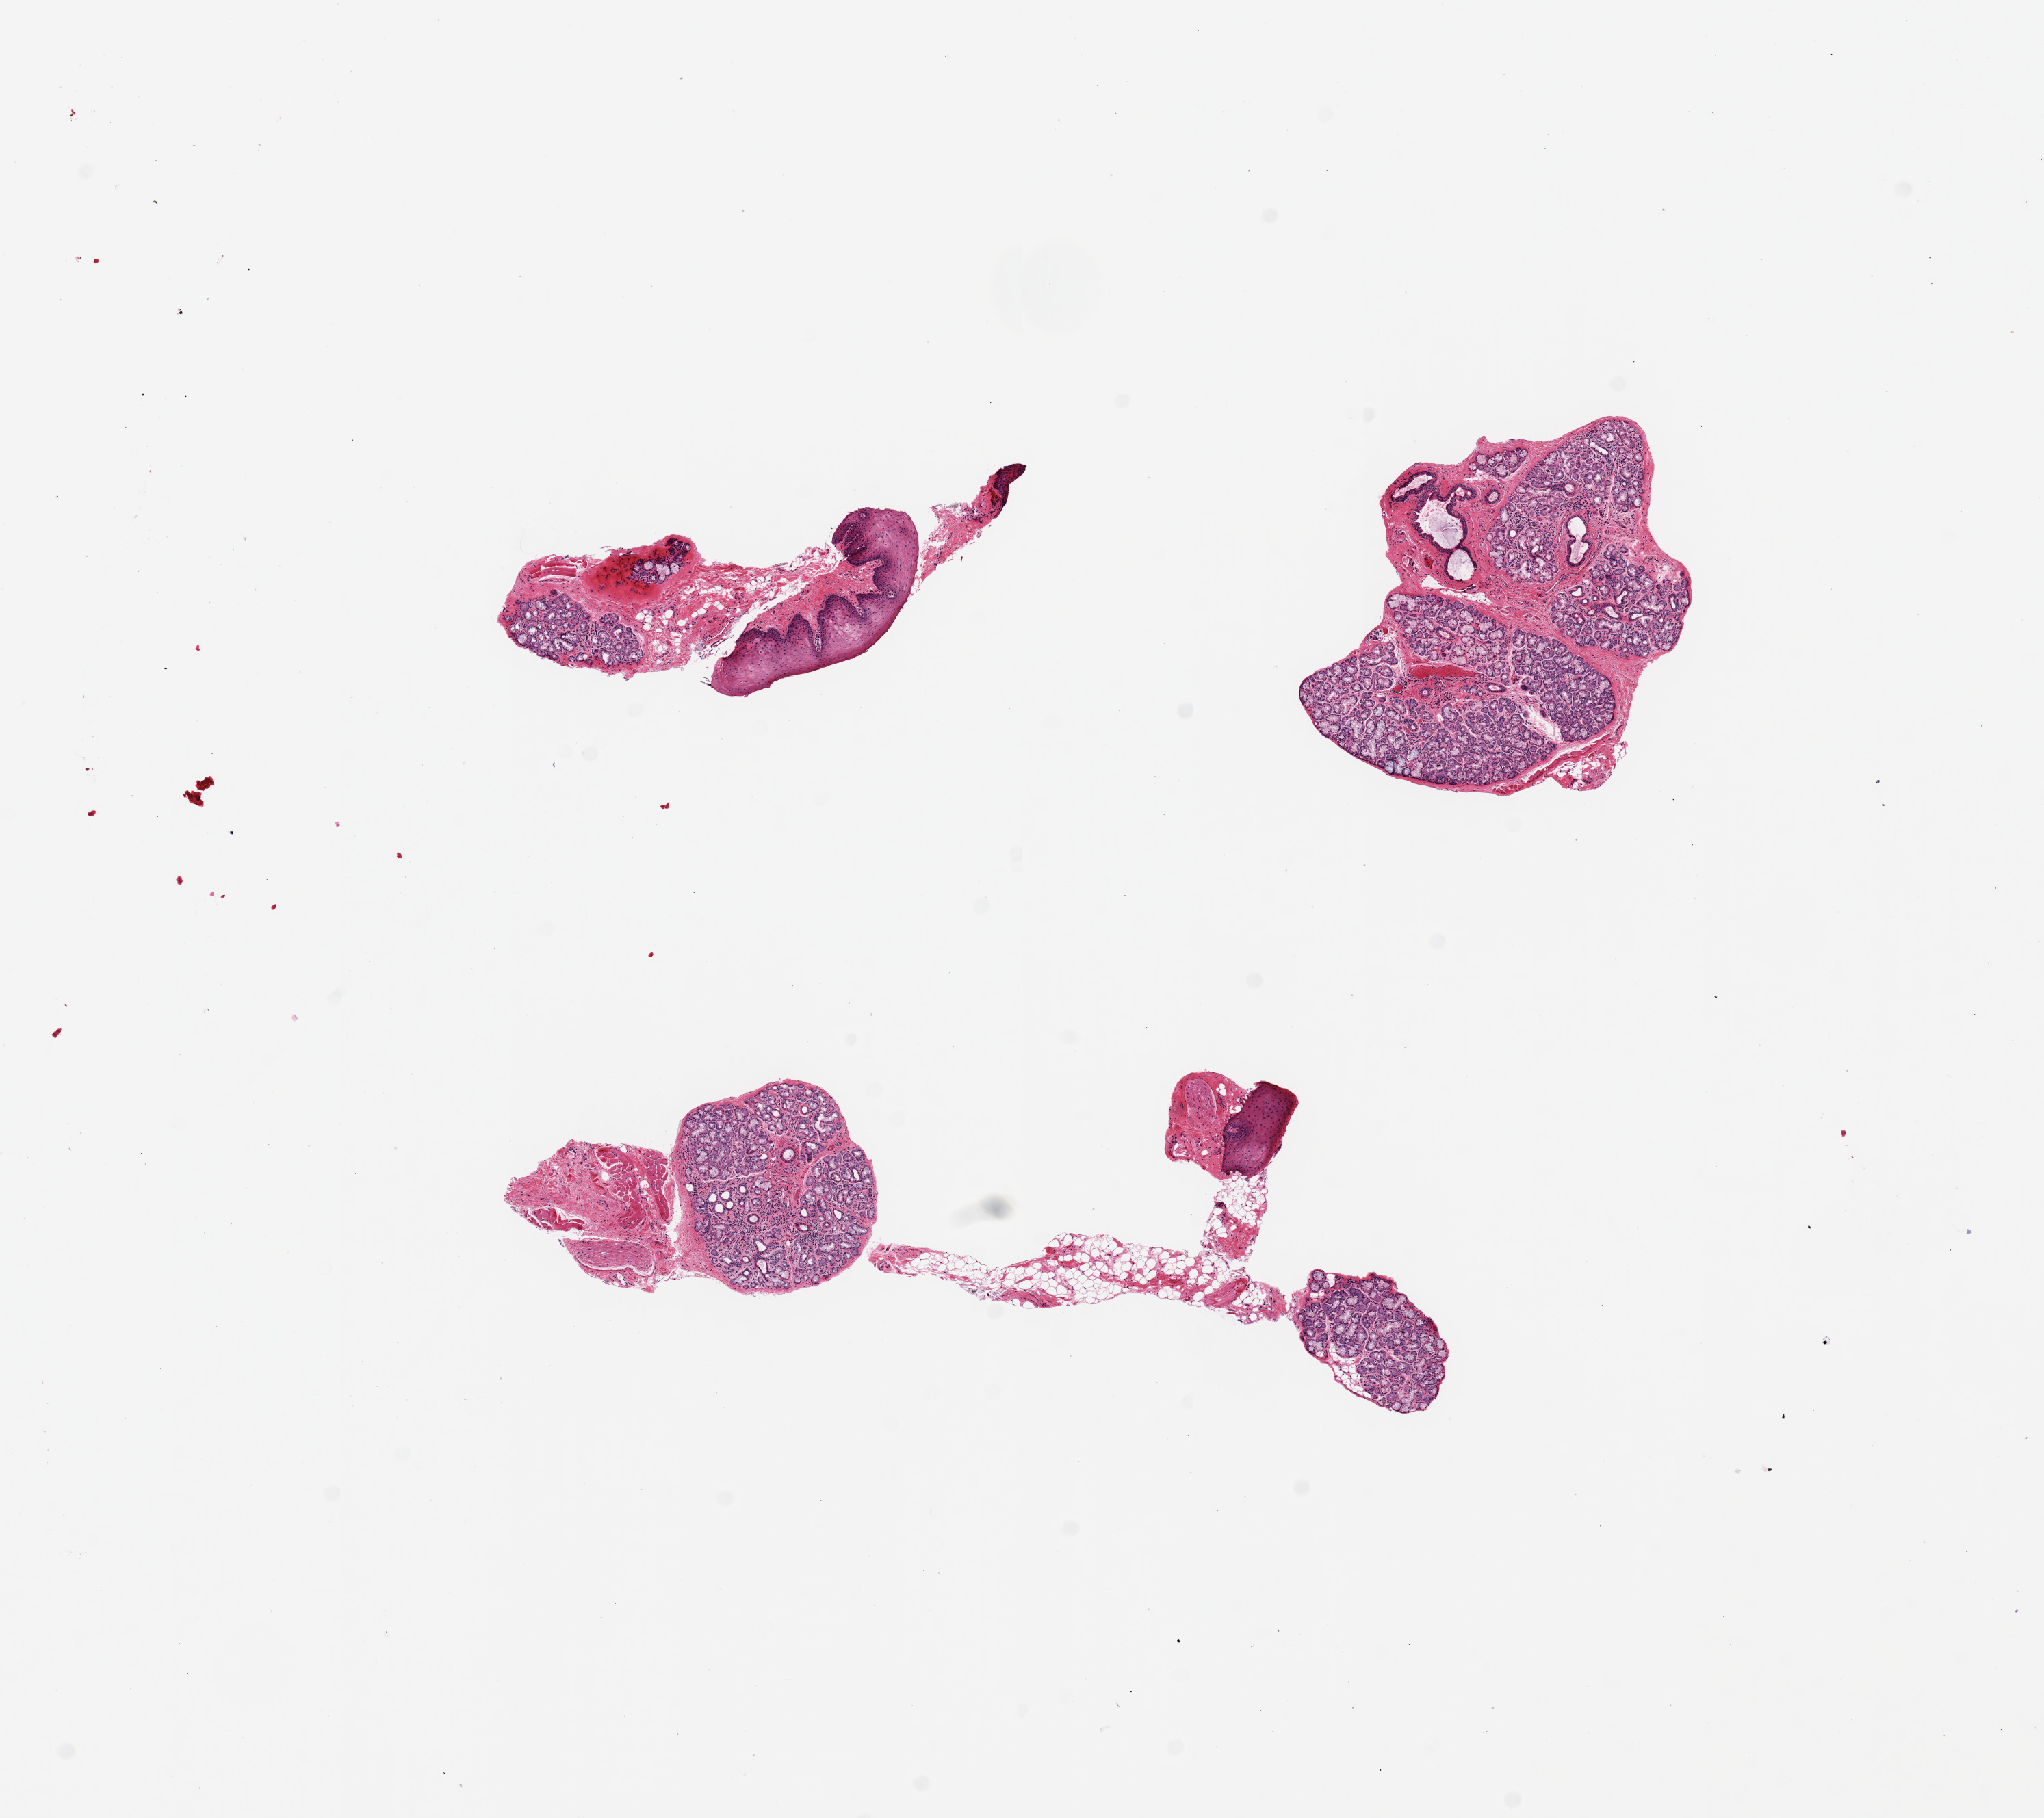
Haematoxylin and eosin whole-slide image — shown as a low-resolution overview of the whole scanned area (about 11.8 x 10.5 mm), PAXgene-fixed paraffin-embedded (PFPE) section, target tissue: minor salivary gland, tissue donor sample. Female donor.
Review note (as recorded): 4 pieces (fragmented), ~70% glandular elements.